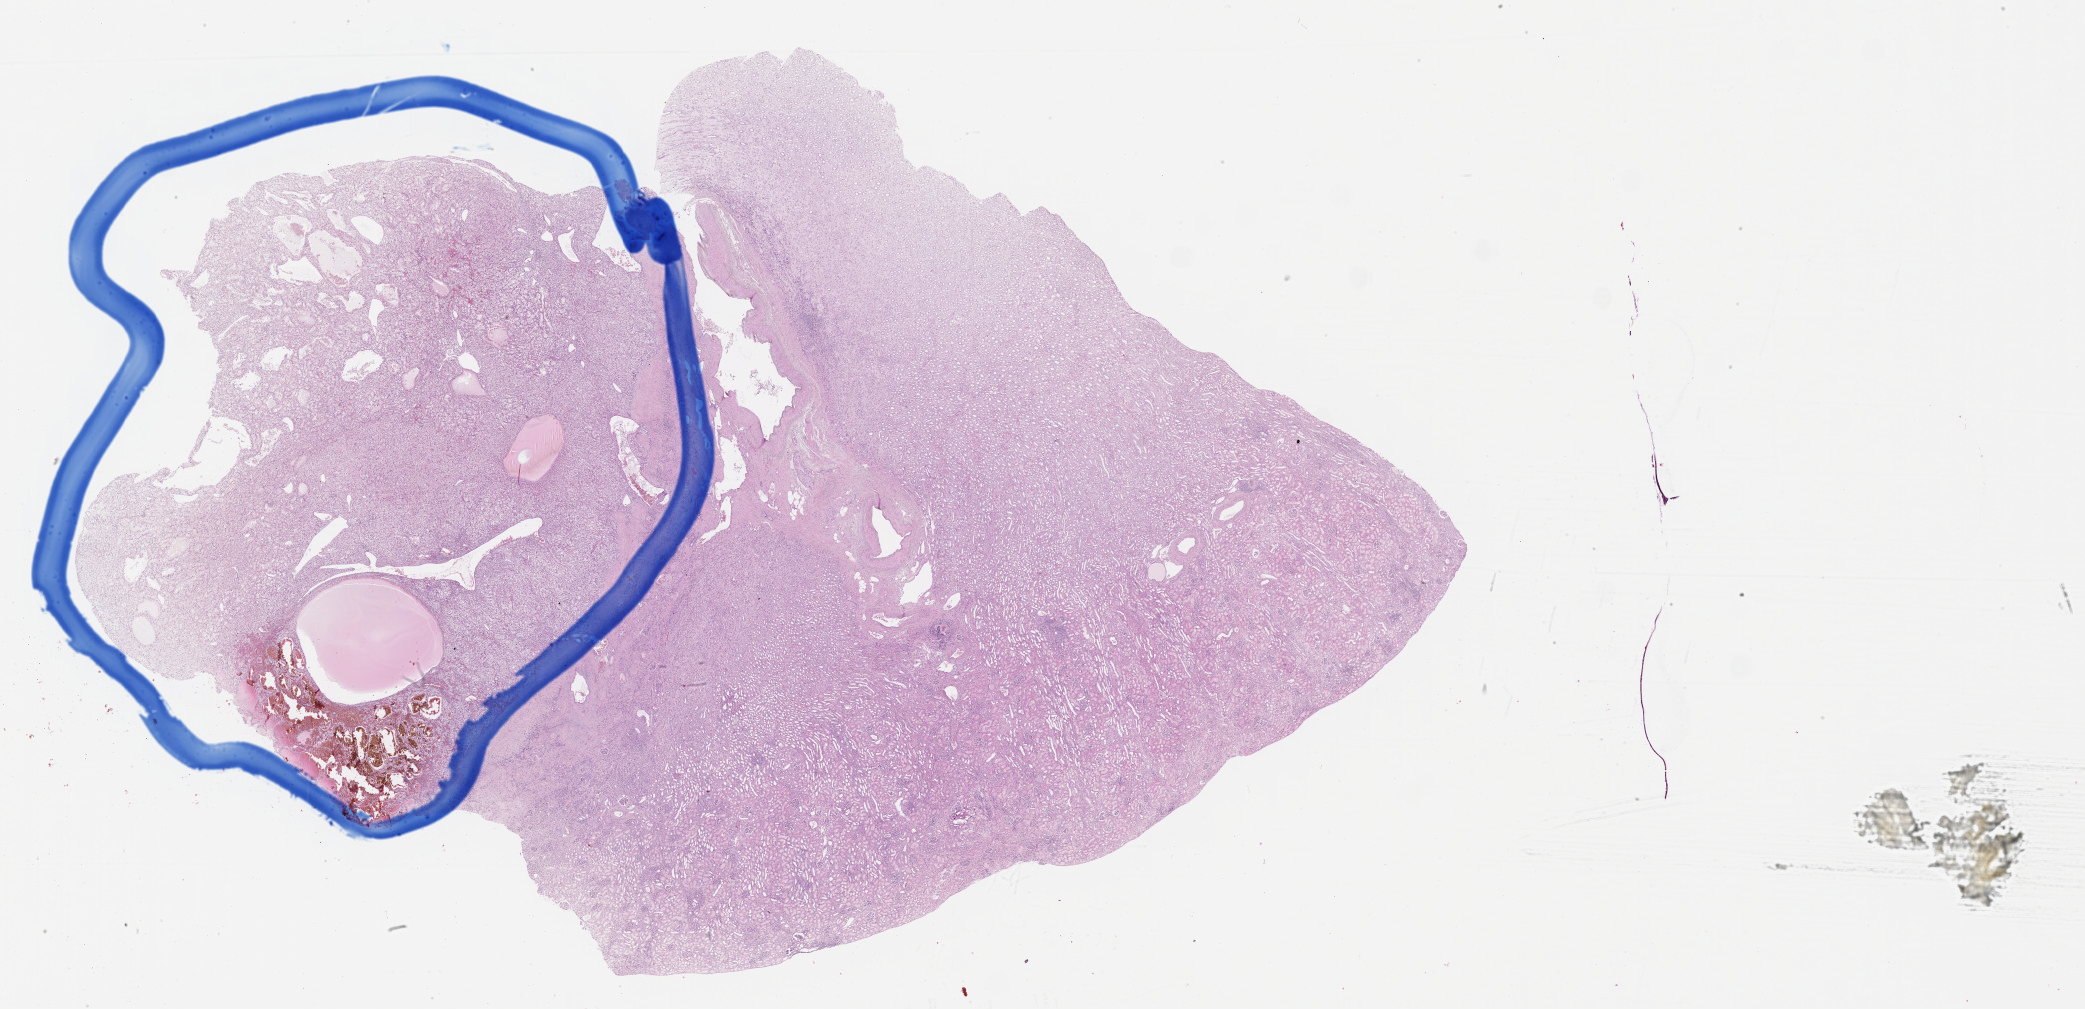
Digitized H&E-stained tissue section (whole slide) — whole scanned area (about 33.7 x 16.3 mm) shown as a low-resolution overview; formalin-fixed paraffin-embedded (FFPE) diagnostic section; sample: primary tumour, kidney. Female, age 59 years at initial diagnosis. Histologic grade: G3 (poorly differentiated).
* histologic diagnosis: Clear cell adenocarcinoma, NOS
* TNM: T1b NX M0
* AJCC pathologic stage: I